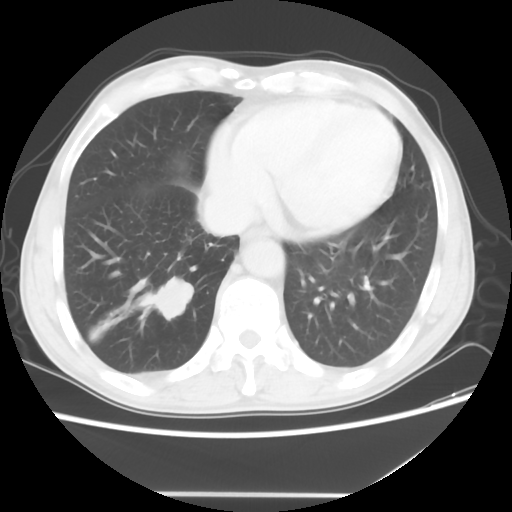
Chest CT, one axial slice. Slice 15 of 56 in the series (ordered by position). Lung window (W 1500 / L -600 HU). 5 mm slice thickness. 512 × 512 image matrix, field of view 344 × 344 mm. Male patient, age 65 years. Case-level facts recorded for this patient, not image findings: clinical TNM (as recorded): T1c N3 M0.
Outlined on this slice (bounding box drawn by a radiologist):
- lung tumour (recorded histology: small cell carcinoma): box from (x=134, y=266) to (x=198, y=325) px